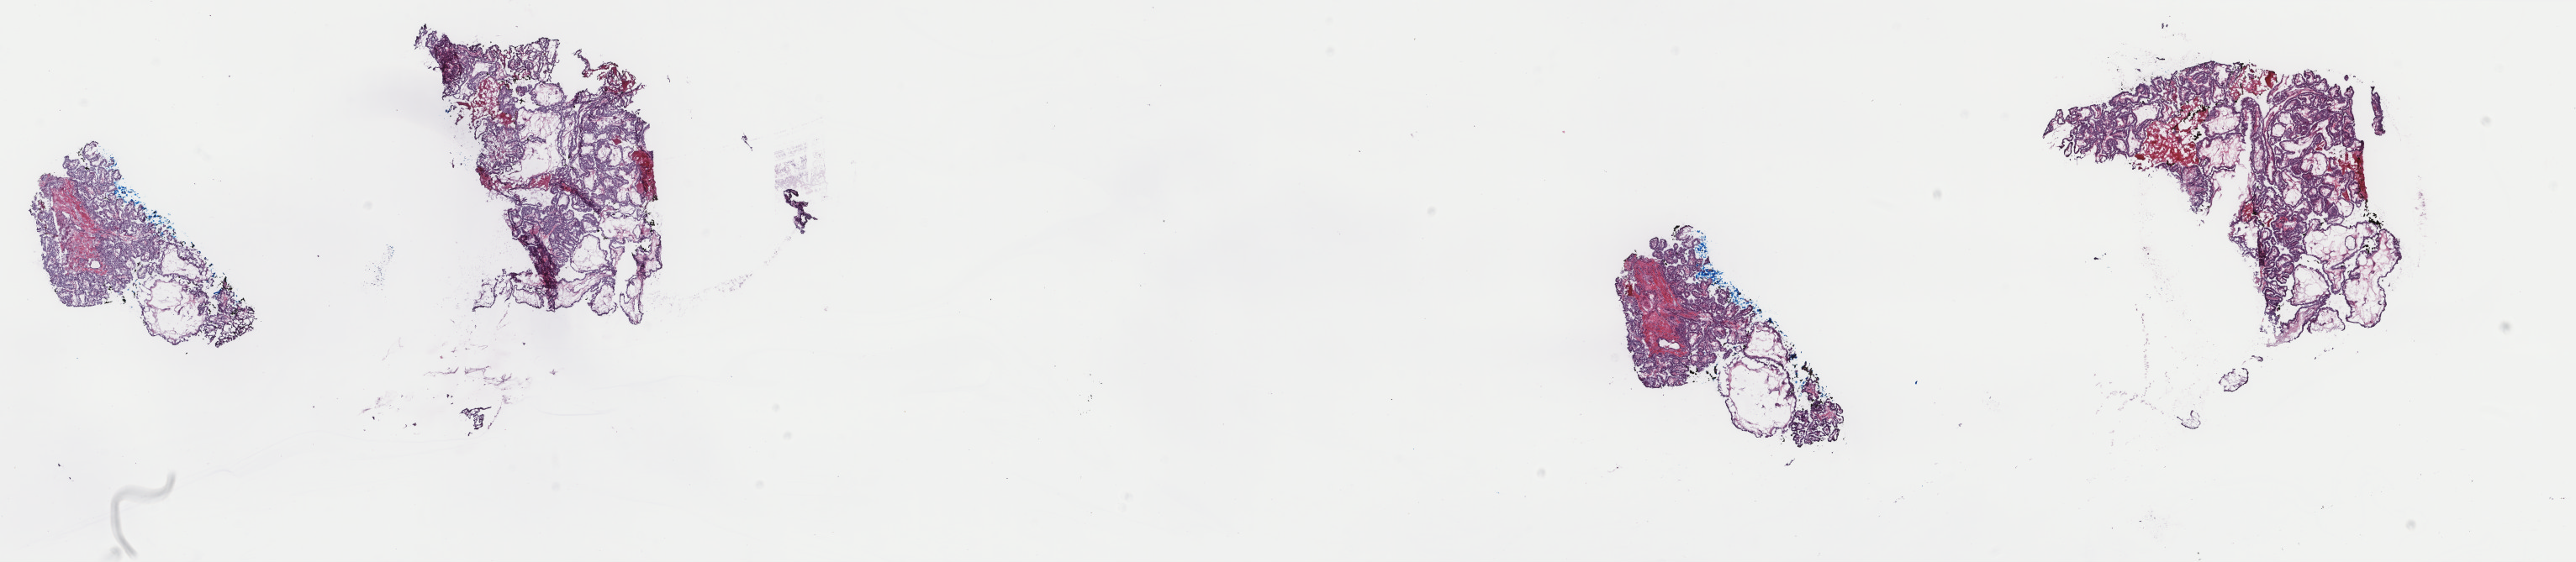
Hematoxylin and eosin (H&E) stained whole-slide image, whole scanned area (about 24.3 x 5.3 mm) shown as a low-resolution overview; frozen section from the top of the tissue portion; thyroid, primary tumour sample. Female, age 21 years at initial diagnosis. Slide review estimates, as recorded: tumour cells 85%, tumour nuclei 85%, normal cells 0%, stromal cells 15%, necrosis 0%. Inflammatory infiltration, as recorded: lymphocyte infiltration 0%, monocyte infiltration 0%, neutrophil infiltration 0%.
• AJCC pathologic stage: I (7th edition)
• pathologic diagnosis: Papillary adenocarcinoma, NOS (thyroid gland)